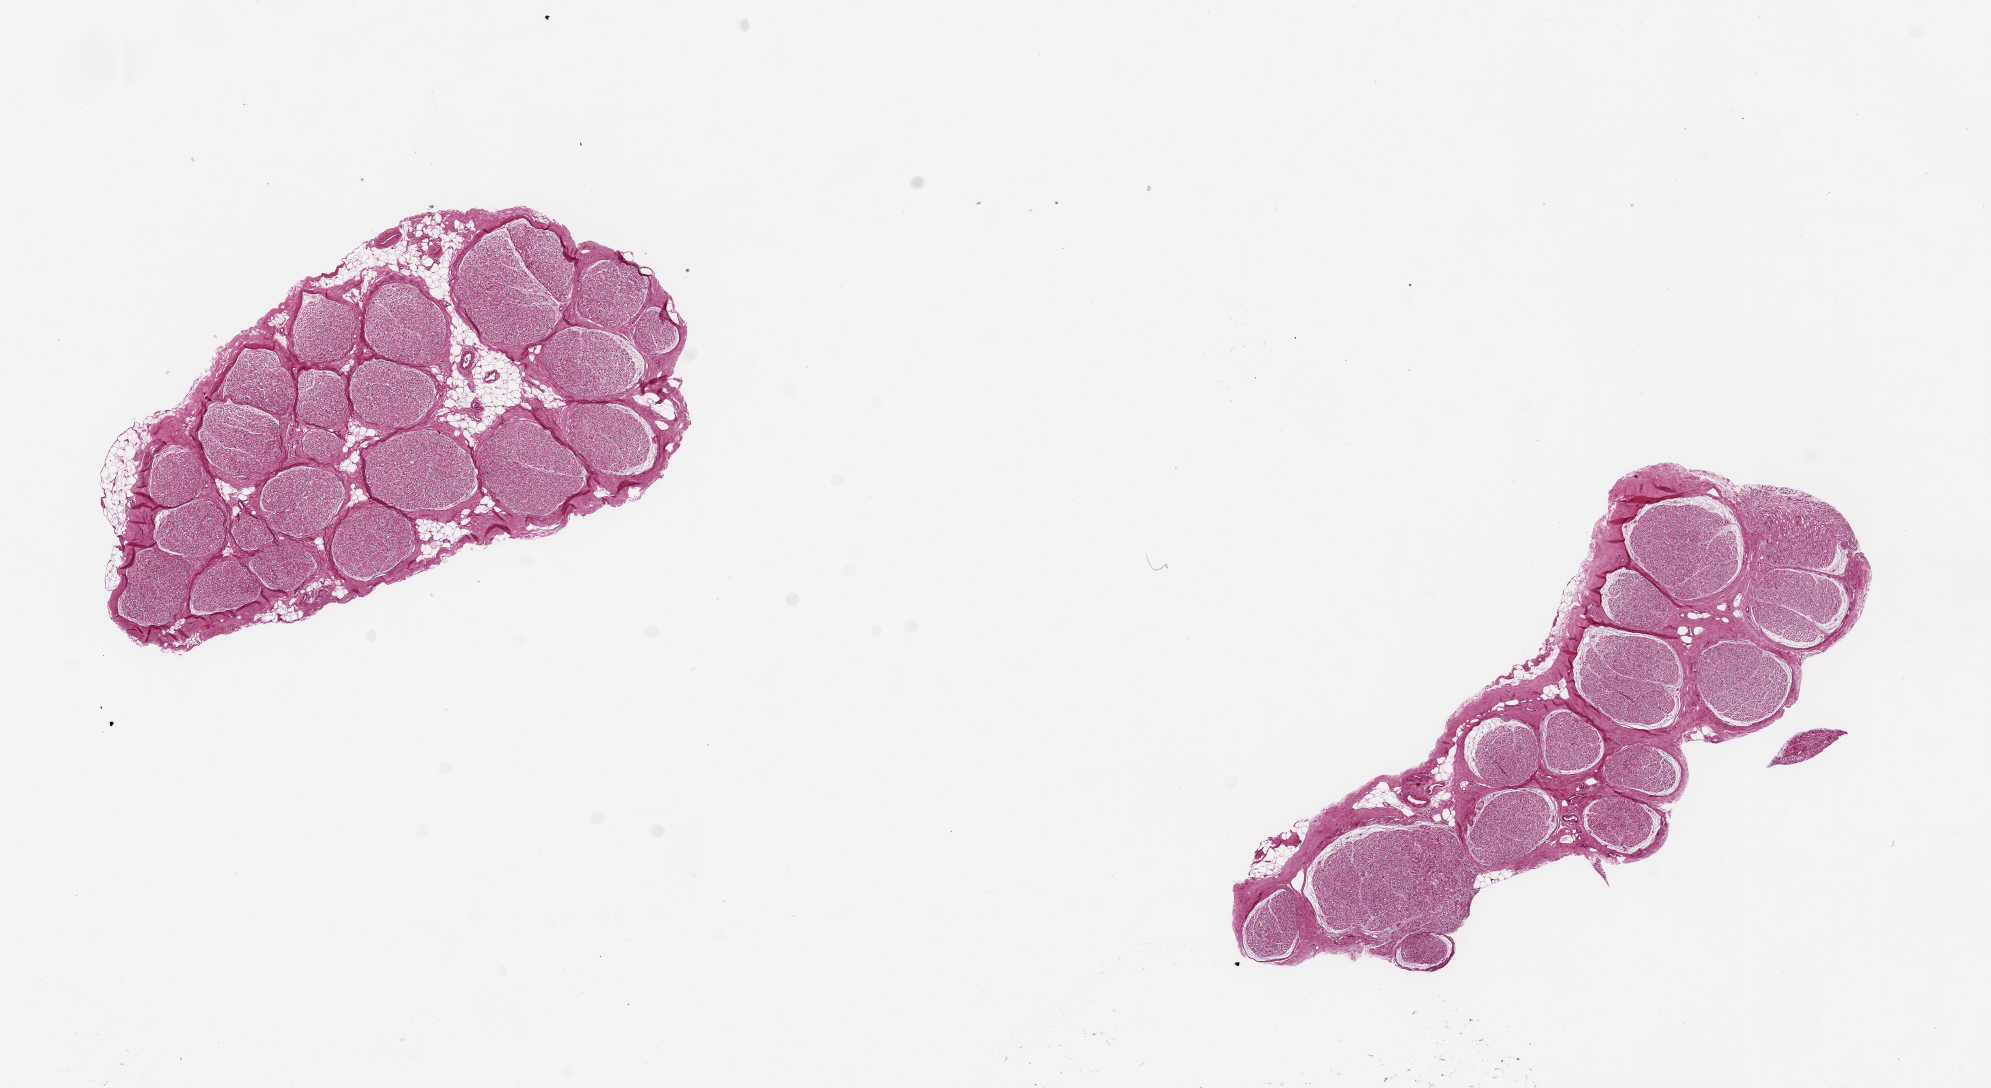
Digitized haematoxylin and eosin-stained section — whole scanned area (about 15.8 x 8.6 mm) shown as a low-resolution overview, PAXgene-fixed paraffin-embedded (PFPE) section, sampled site (target tissue): tibial nerve, donor tissue sample. Donor sex: female.
Review note (as recorded): 2 pieces, 5x3 & 6x3mm; good clean specimens, adherent fat.